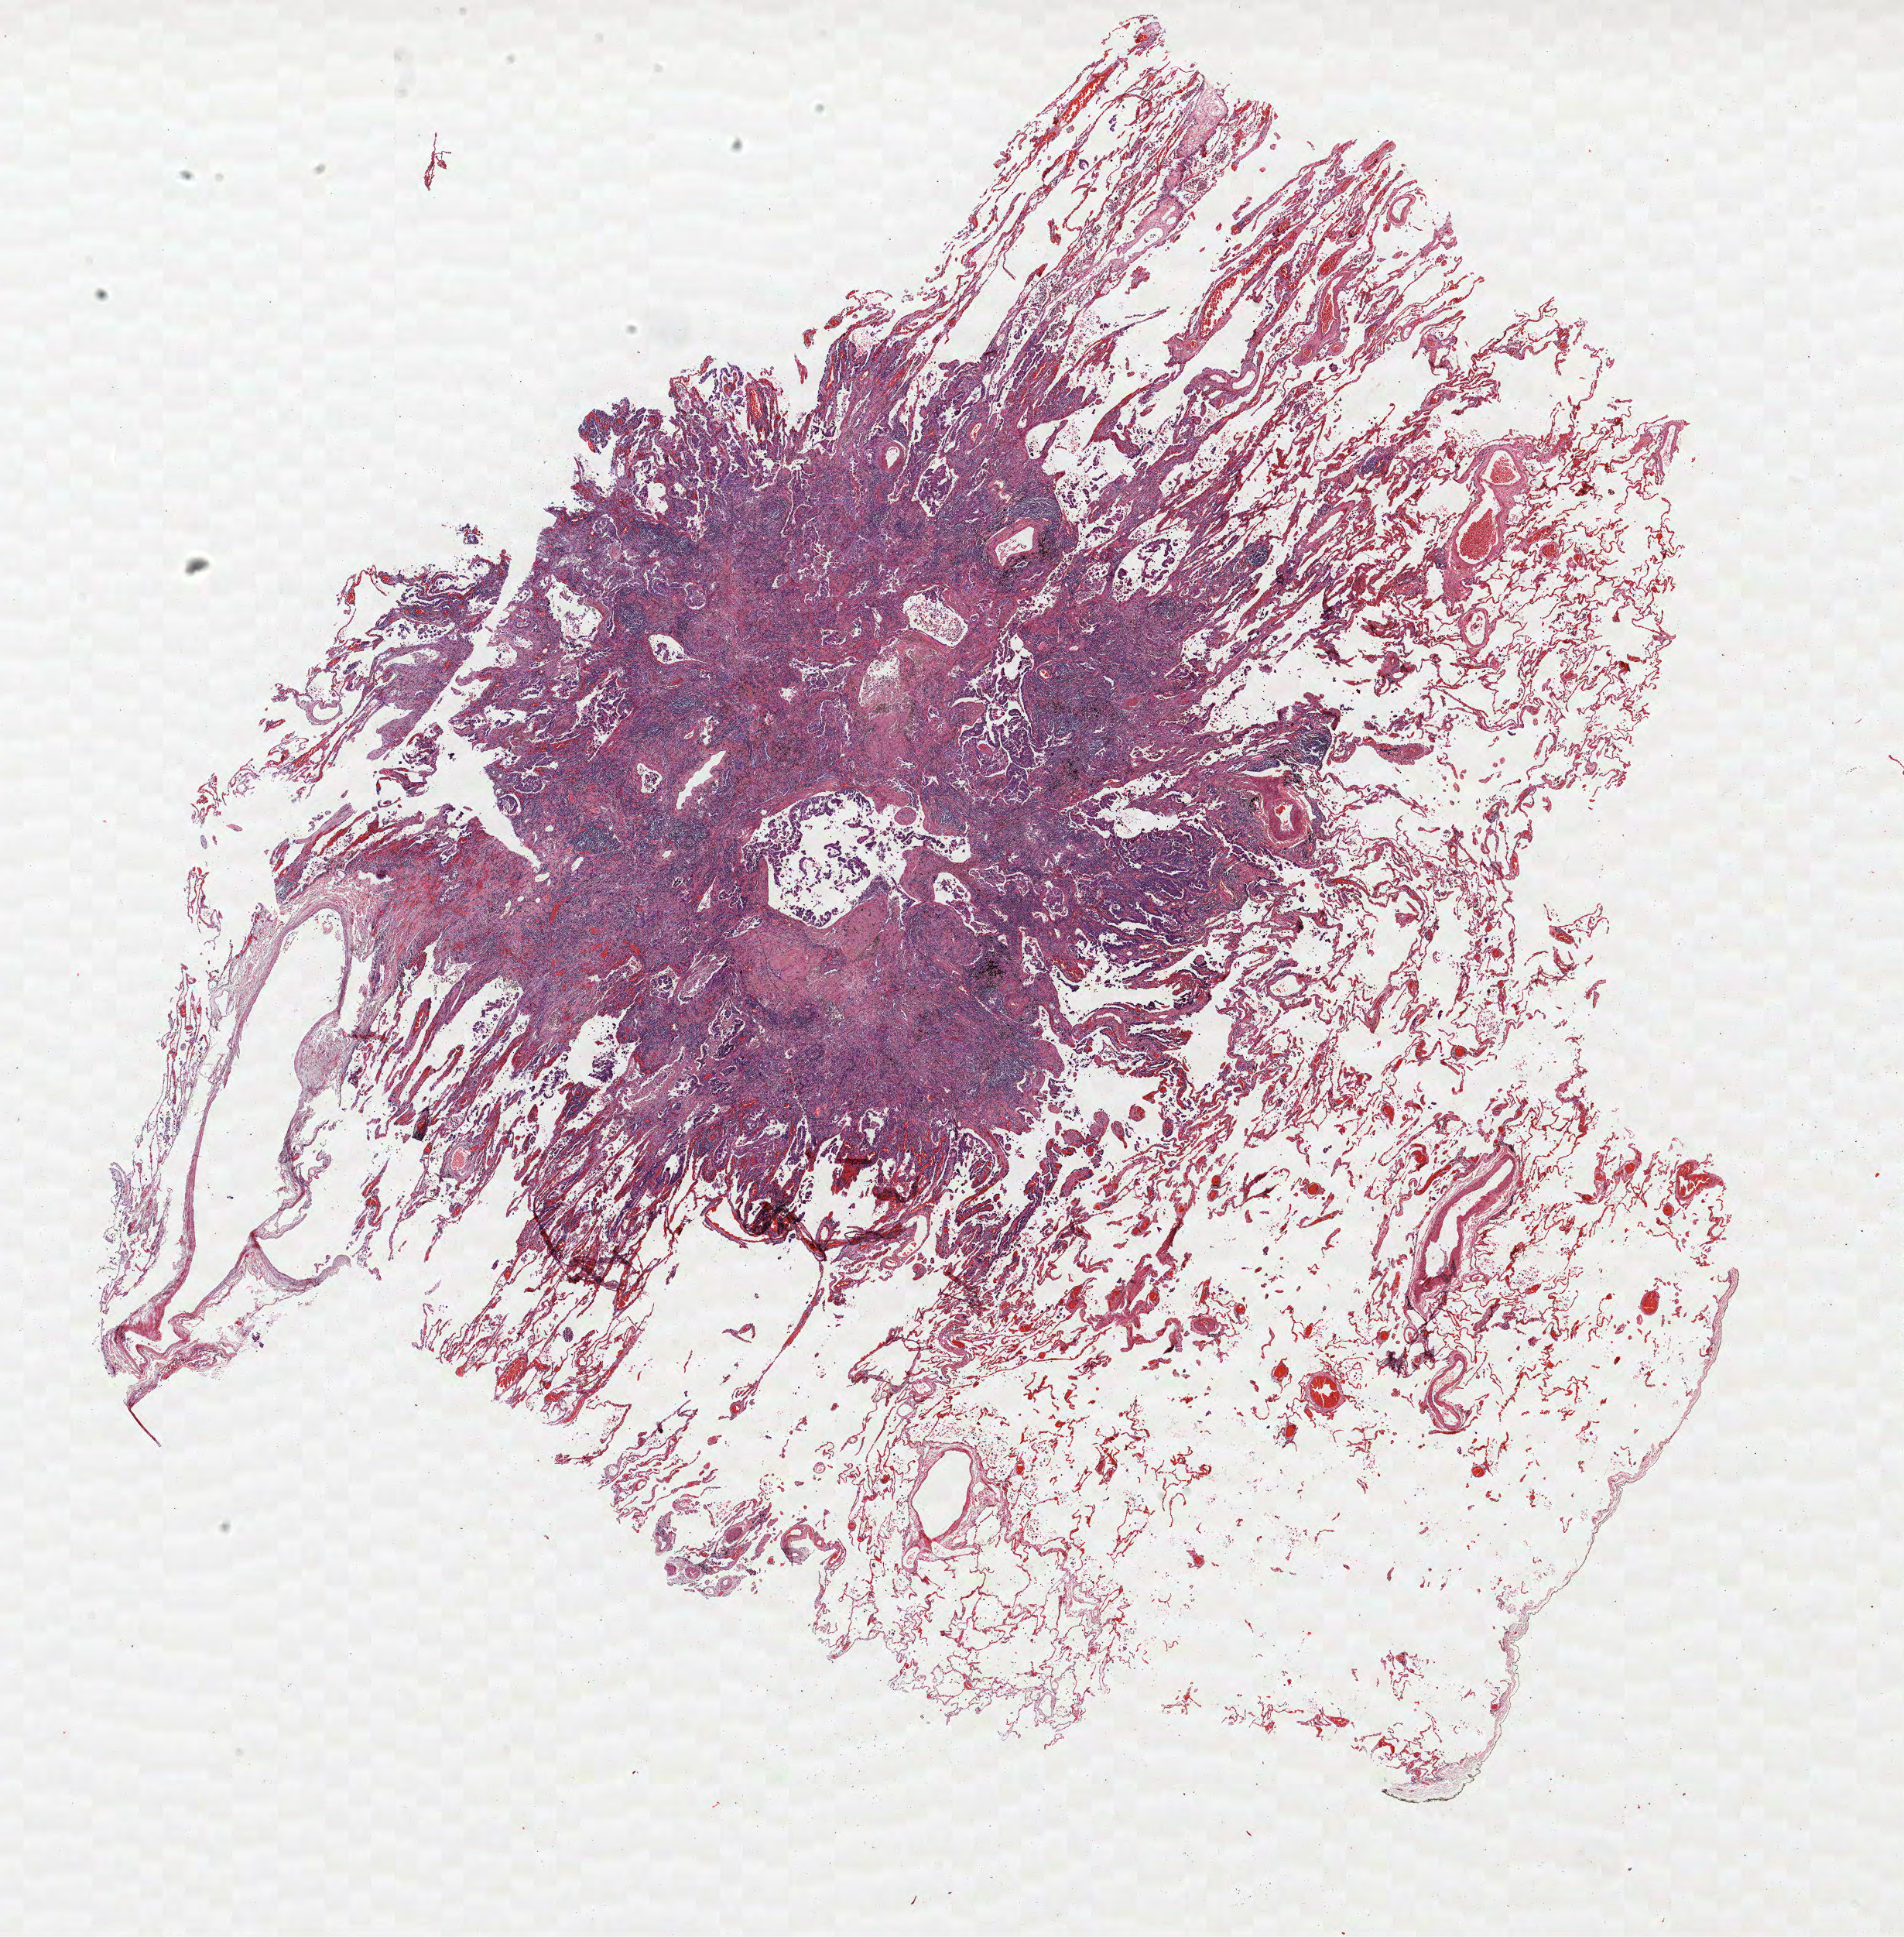
Whole-slide histology image, H&E-stained, low-resolution overview of the scanned area, about 19.7 x 20.0 mm, FFPE section, lung tissue. Male, age 62 at enrolment. Current smoker at enrolment.
Participant's lung-cancer diagnosis: Bronchiolo-alveolar adenocarcinoma, NOS.